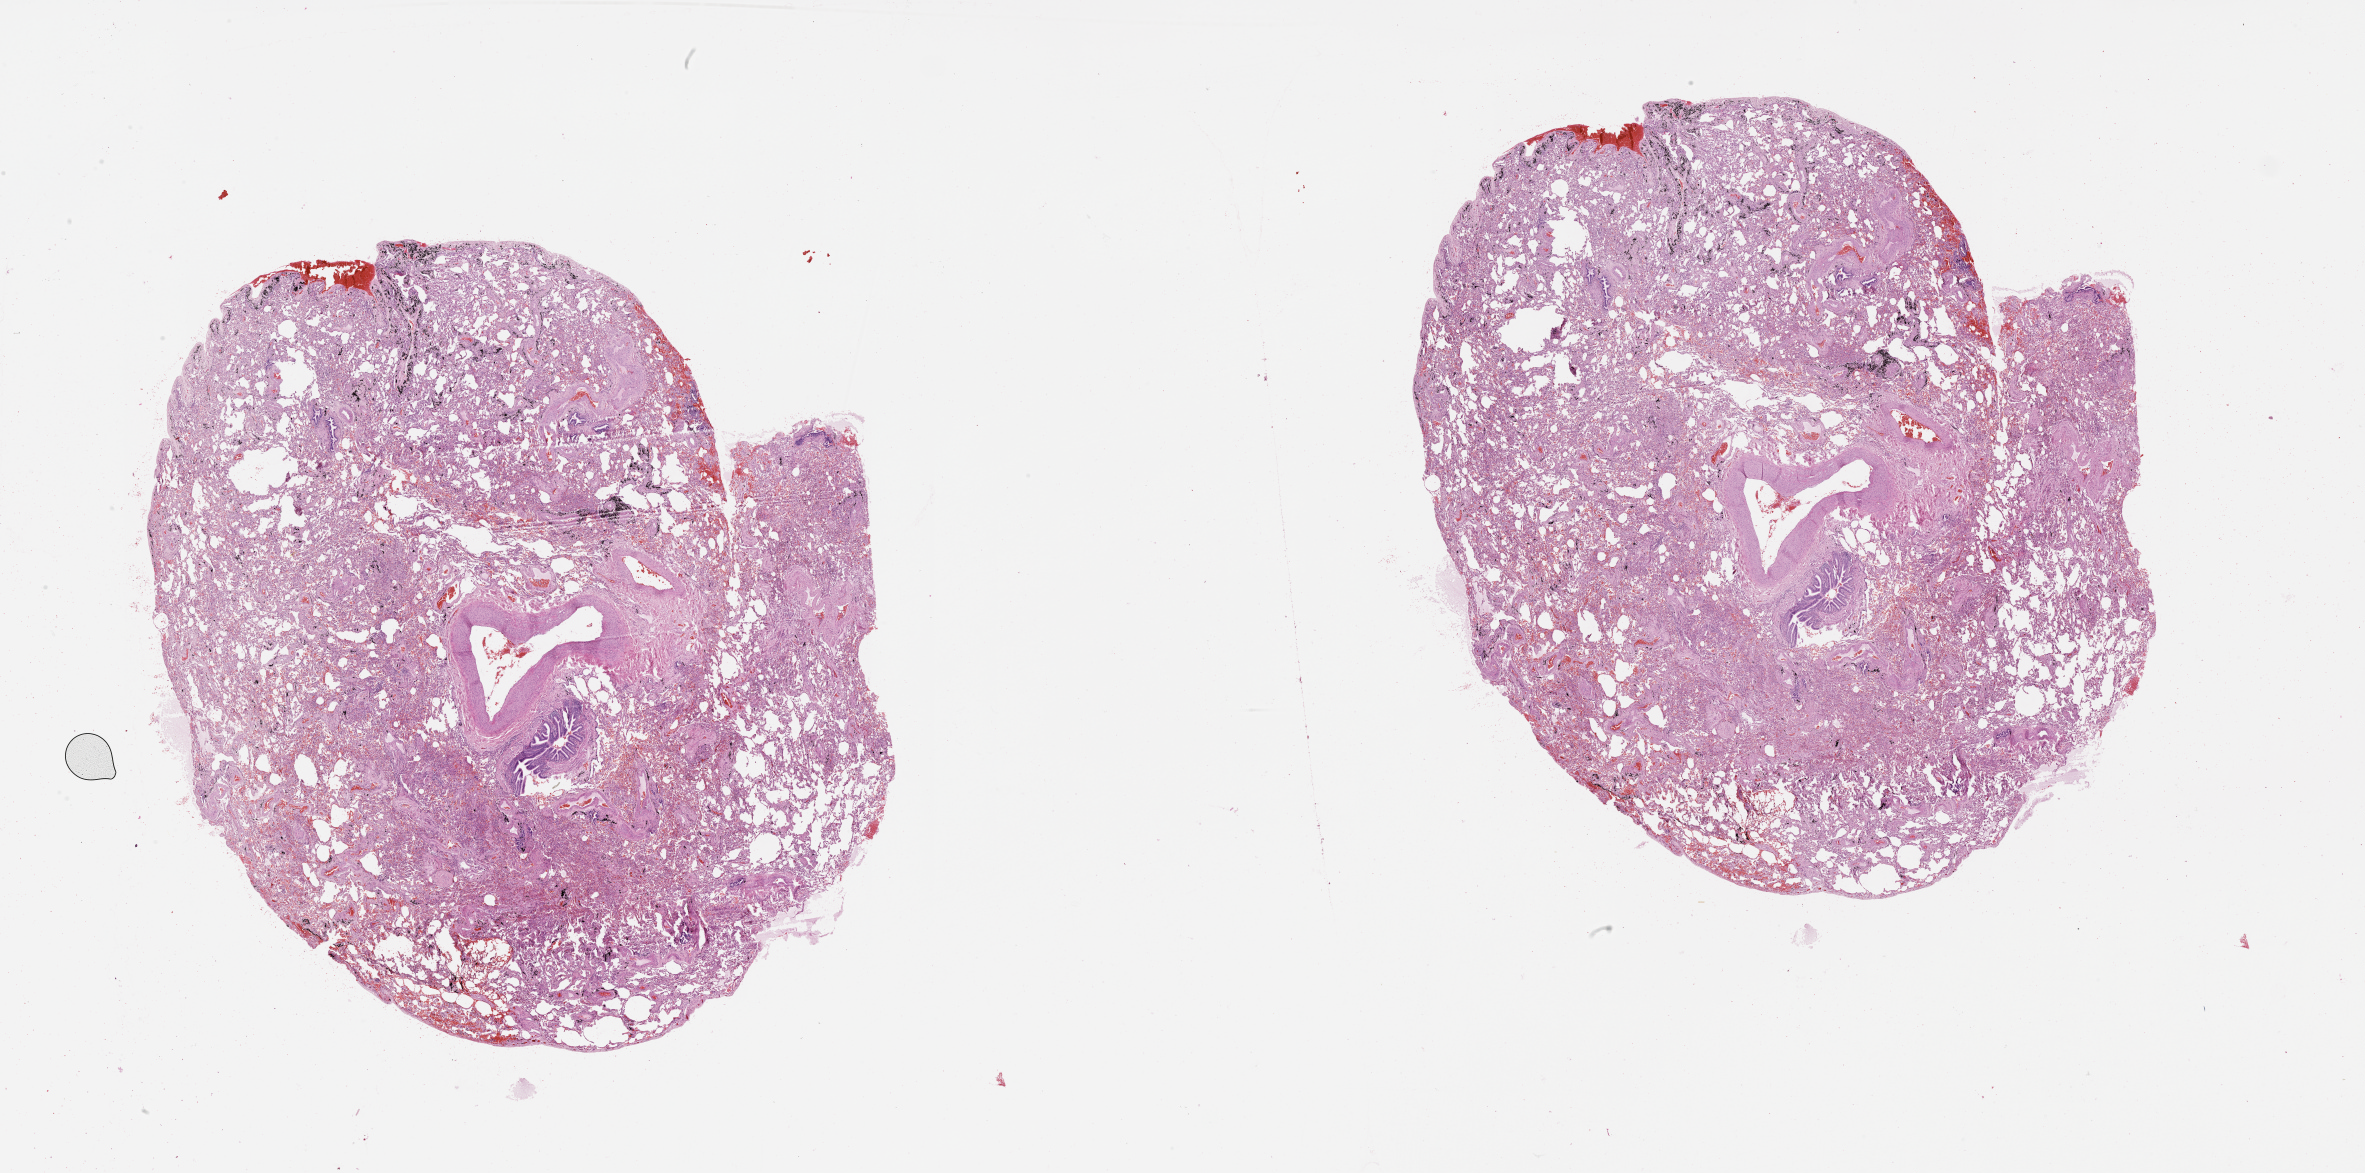
Whole-slide histology image, H&E — low-resolution overview of the scanned area, about 38.1 x 18.9 mm (acquisition: 20x scan). Lung, tissue type not recorded.
Patient diagnosis (cohort enrolment): squamous cell carcinoma (lung).